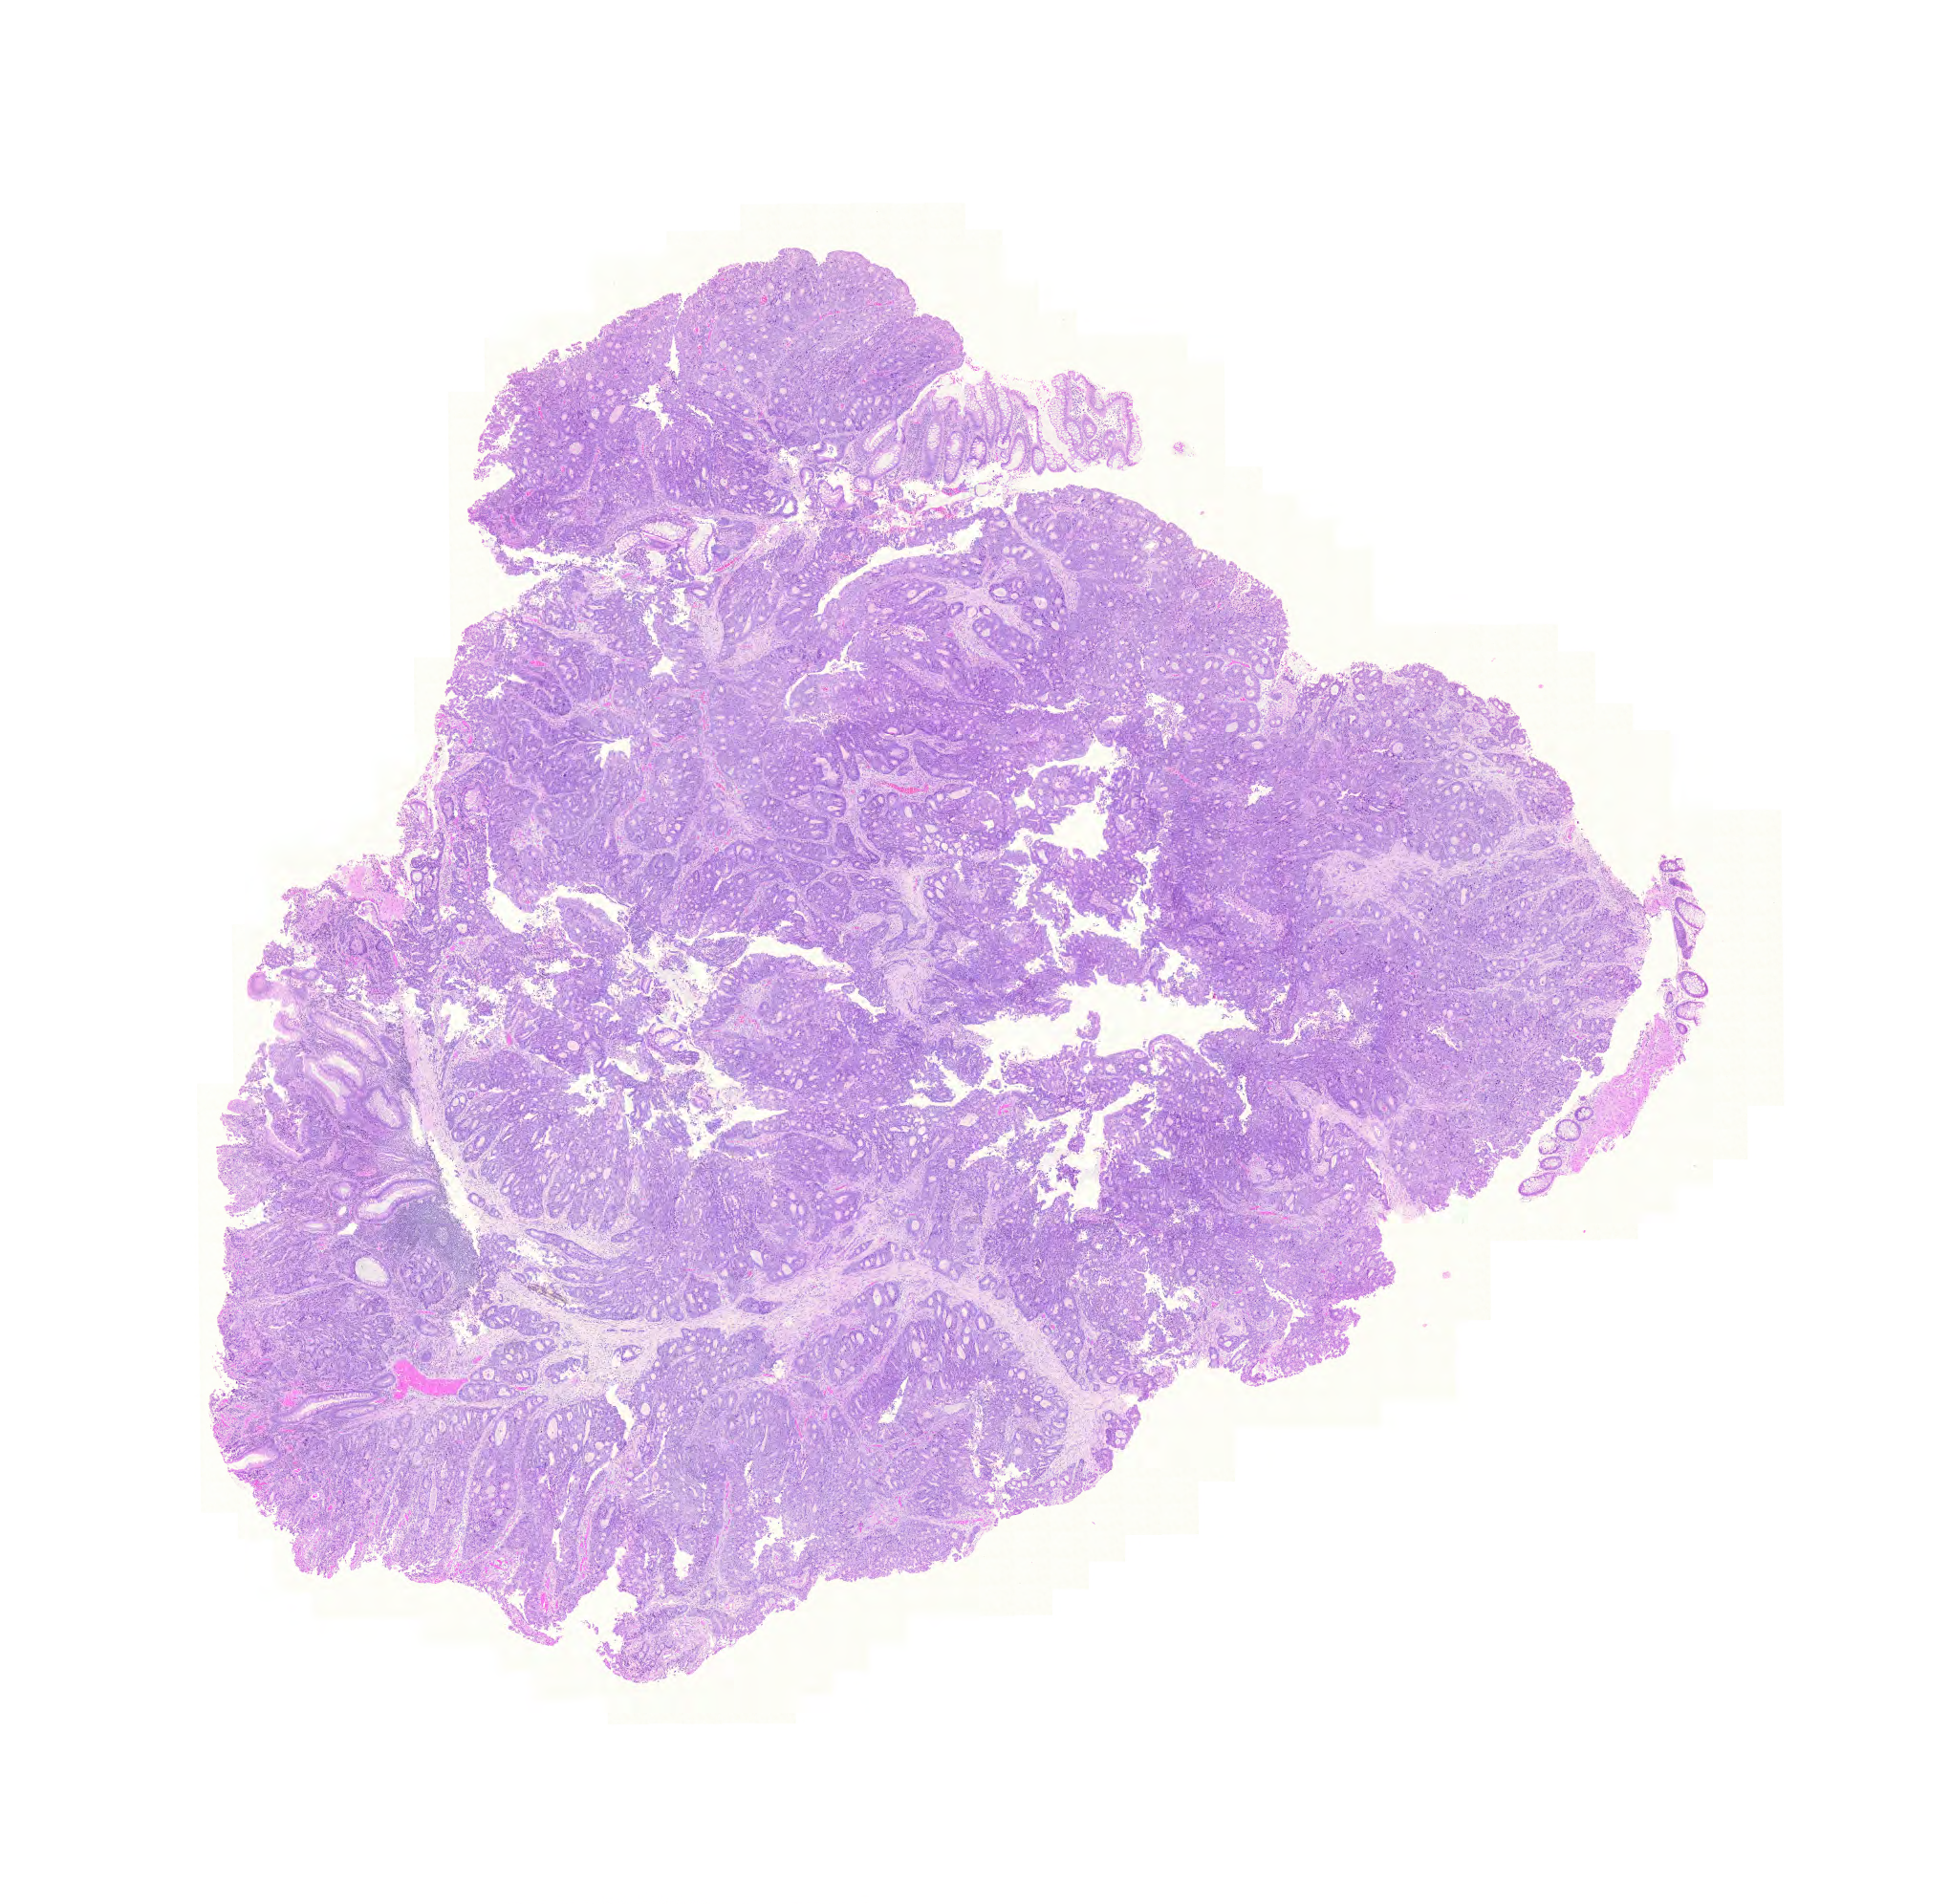
Whole-slide histology image, H&E-stained, low-resolution overview of the scanned area, about 15.2 x 14.8 mm (from a 20x scan); FFPE section; sample: primary tumour, rectum. Male patient; age at initial diagnosis 60 years.
Histologic diagnosis: Adenocarcinoma, NOS.